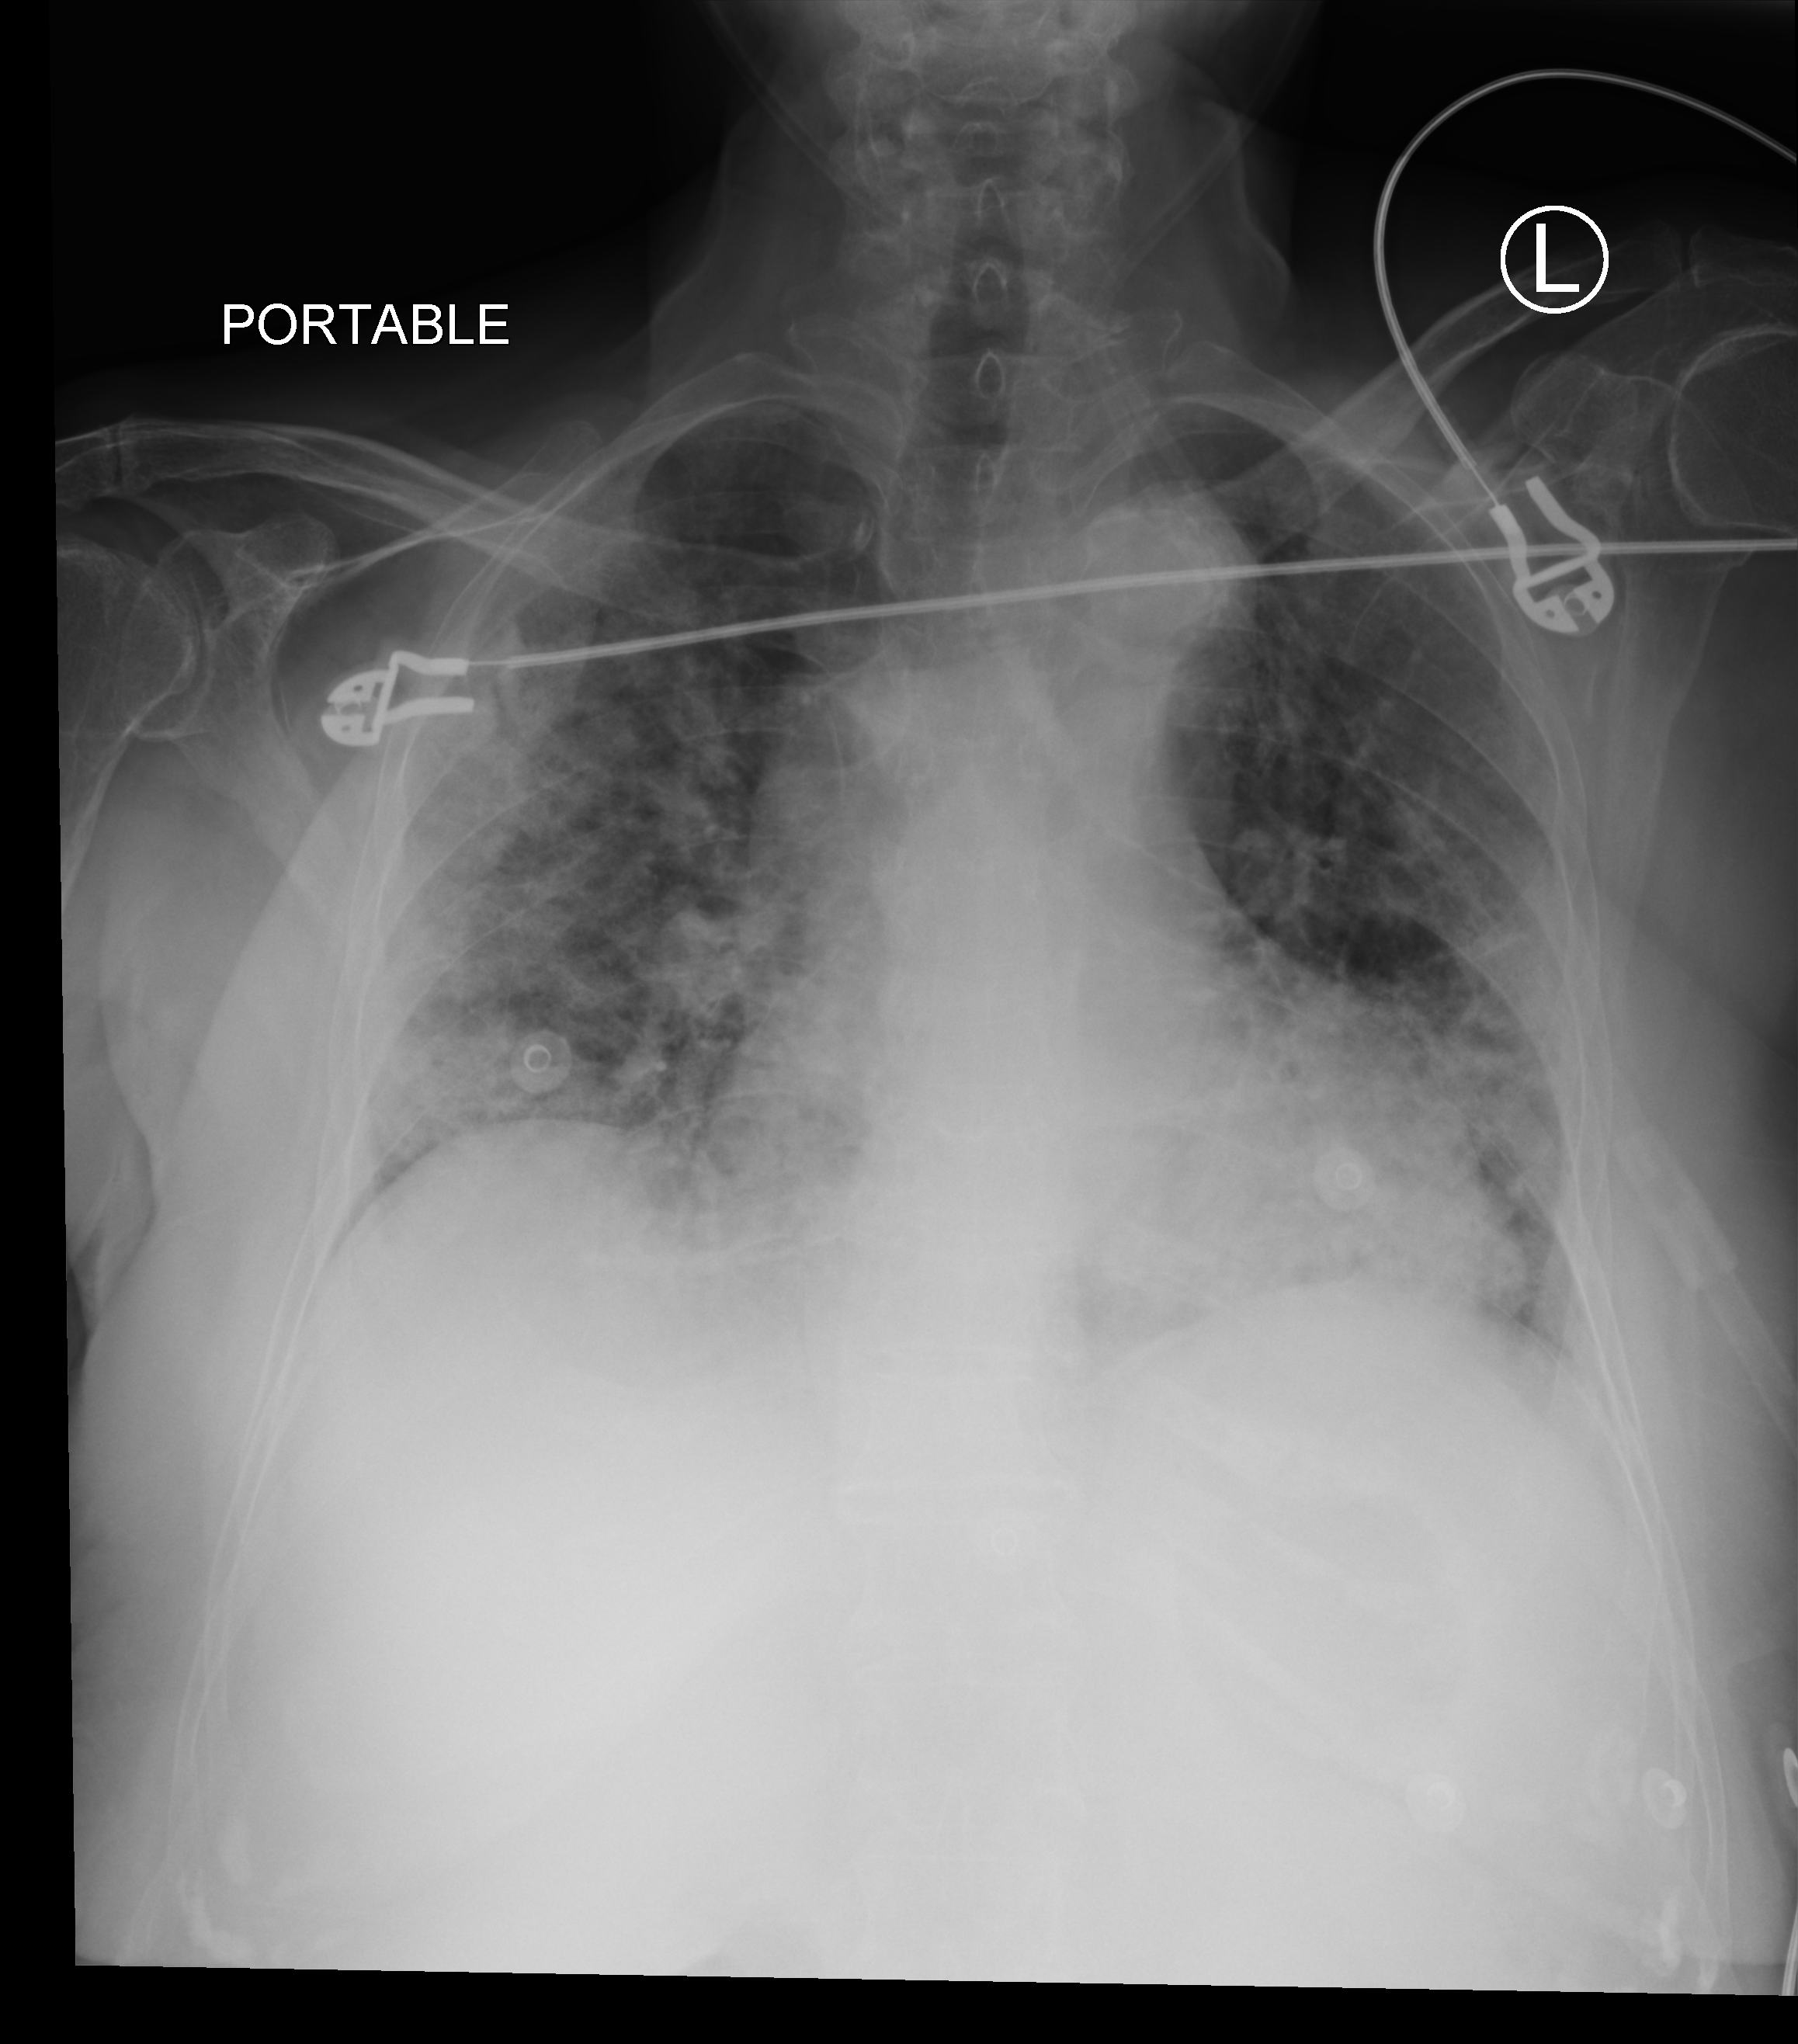
Bedside chest radiograph (computed radiography), anteroposterior (AP) projection. Female patient hospitalised with COVID-19, age 75–90 years.
Admission-level facts for this patient (not findings on this image; timing relative to this image not recorded): diabetes (admission record): yes; length of hospital stay: 15 days; admitted to intensive care during this hospital stay: no.